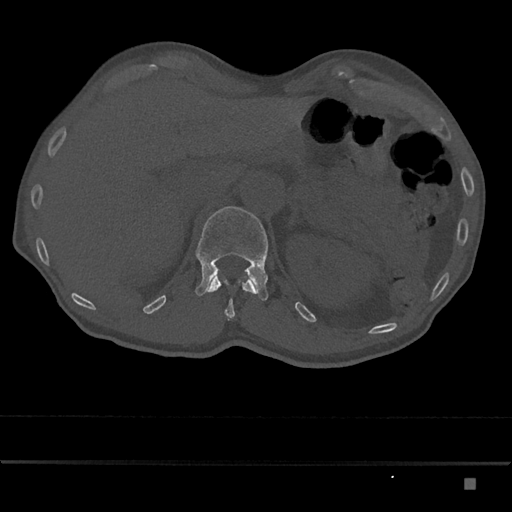
CT including the spine, one axial slice. Position 573 of 797 along the scan axis. Reconstruction kernel Br40s/3. 120 kVp. Bone window (W 1800 / L 400 HU). 512 × 512 image matrix, field of view 390 × 390 mm. Patient: male, 72 years. From the clinical record (not read from this slice): primary cancer: prostate.
Annotated regions visible in this slice (semi-automatic segmentation, software-assisted and operator-edited):
- L1 vertebra: bounding box [x1, y1, x2, y2] px = [195, 206, 268, 301]
- T12 vertebra: [205, 276, 256, 318]